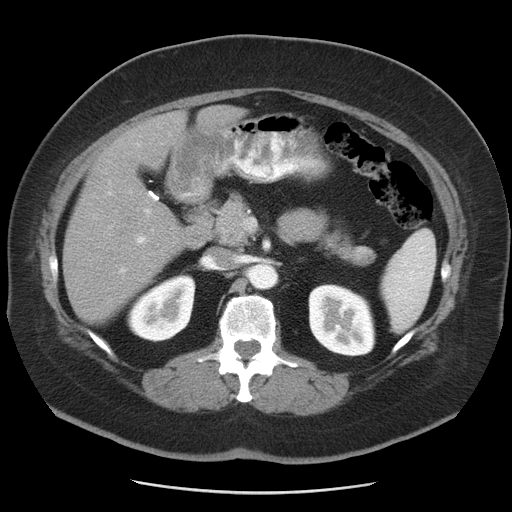
Contrast-enhanced abdominal CT, one axial slice; position 24 of 55 along the scan axis; intravenous contrast given; soft-tissue window (W 400 / L 40 HU); 5 mm slice thickness; 512 × 512 image matrix. Female patient, age 52 years. Case-level facts recorded for this patient, not image findings: diagnosis: colorectal cancer liver metastases, imaged before liver resection; multiple liver metastases: yes; largest metastasis: 2.5 cm; chemotherapy before resection: no.
Outlined on this slice (outlined manually by an expert reader):
- liver: bounding box (x1, y1, x2, y2) in pixels: (63, 109, 242, 323)
- planned liver remnant (the part of the liver to remain after resection): (63, 195, 187, 323)
- portal vein (with intrahepatic branches): (104, 142, 155, 272)